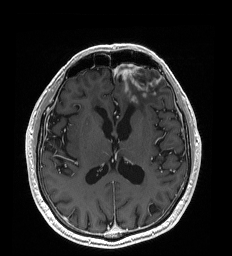
Brain MRI from a brain-tumour surgery series, one axial slice; T1-weighted post-contrast; 232 × 256 image matrix, field of view 227 × 250 mm. Case-level facts recorded for this patient, not image findings: histopathology: Glioblastoma; WHO grade: 4; IDH mutation: no.
Outlined on this slice (outlined manually by an expert reader):
- tumour: bounding box (x1, y1, x2, y2) in pixels: (127, 95, 137, 102)